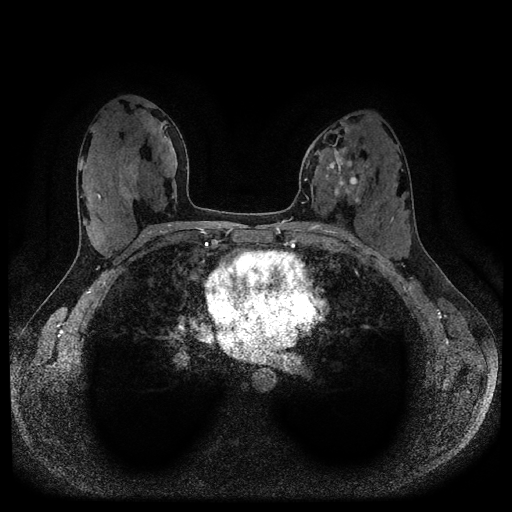
Breast MRI (dynamic contrast-enhanced, multi-phase), one axial slice. Position 54 of 116 along the scan axis. Dynamic contrast-enhanced series, time point 2 of 5 at this slice position (early post-contrast). 1.5 T. TE 2.6 ms, TR 5.3 ms. 512 × 512 image matrix. Patient: female, 33 years.
Outlined on this slice (semi-automatic segmentation, software-assisted and operator-edited):
- breast lesion (labelled 'tumour' in the annotation; benign lesions carry a separate 'benign' label): bounding box <324,148,360,204> (left, top, right, bottom; pixels)